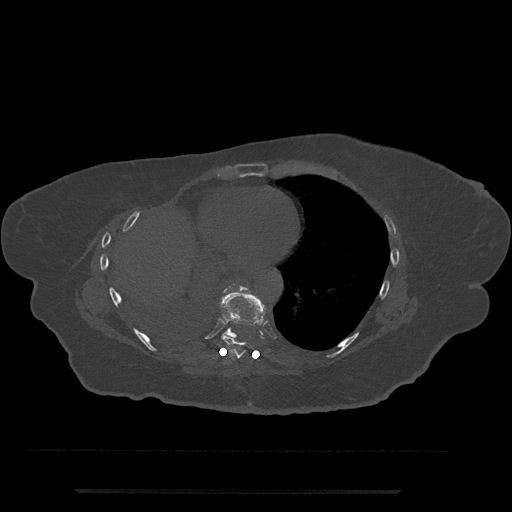
CT including the spine, one axial slice; slice 376 of 797 in the series (ordered by position); 120 kVp; bone window (W 1800 / L 400 HU); 512 × 512 image matrix. Patient: female, 51 years. From the clinical record (not read from this slice): primary cancer: neuro.
Annotated regions visible in this slice (semi-automatically segmented with operator editing):
- T8 vertebra: bounding box [x1, y1, x2, y2] px = [220, 284, 265, 359]
- T9 vertebra: [218, 284, 264, 339]